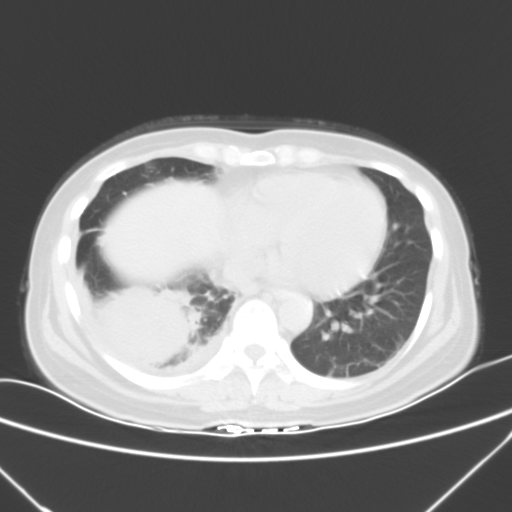
Chest CT, one axial slice; position 15 of 53 along the scan axis; lung window (W 1500 / L -600 HU); 5 mm slice thickness; 512 × 512 image matrix. Patient: female, 42 years. Case-level facts recorded for this patient, not image findings: clinical TNM (as recorded): T3 N0 M1c.
Outlined on this slice (rectangle marked by the reading radiologist):
- lung tumour (recorded histology: adenocarcinoma): bounding box <92,277,199,374> (left, top, right, bottom; pixels)